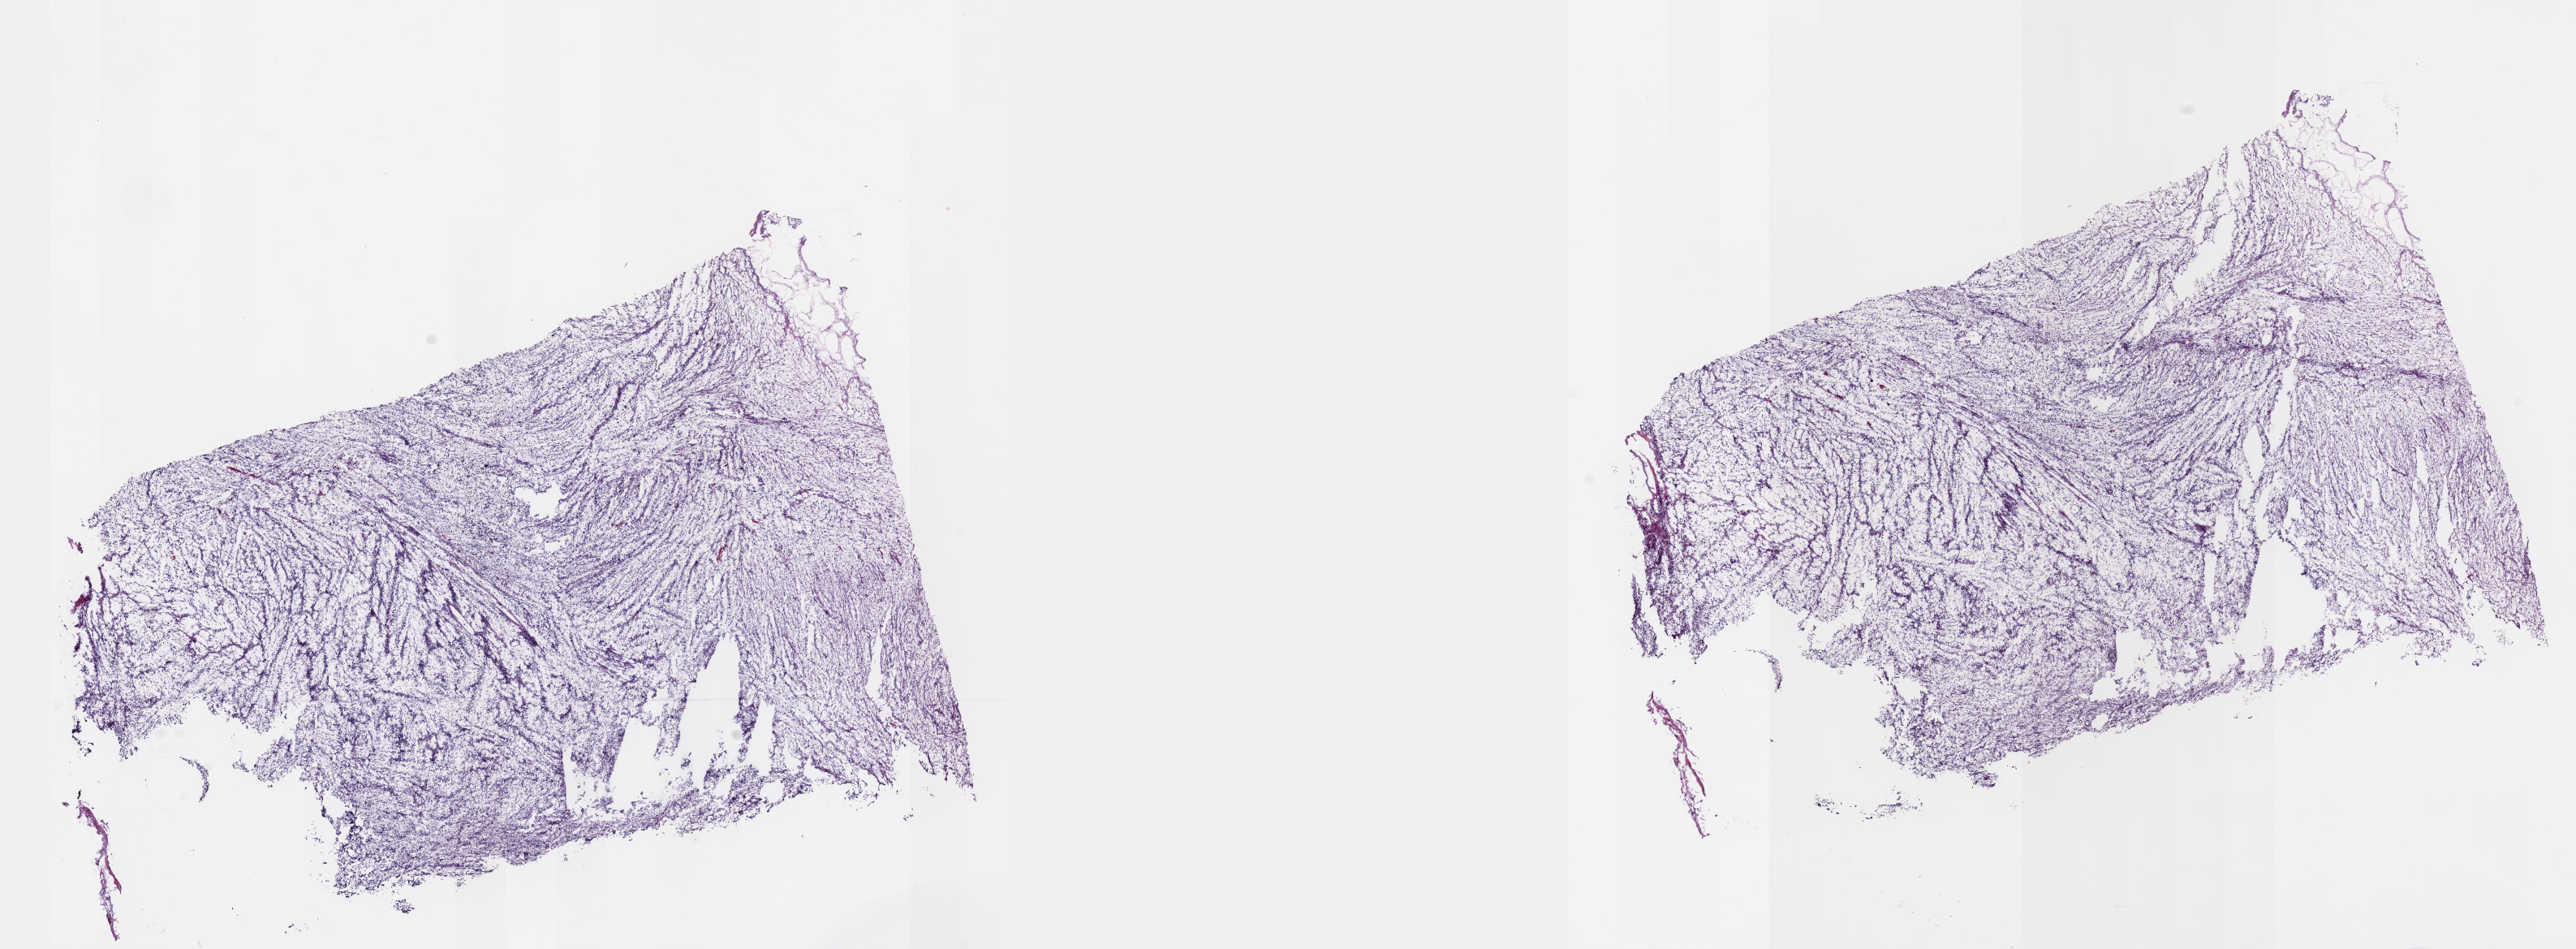
H&E-stained whole-slide image, a low-resolution overview of the entire scanned area, about 25.7 x 9.4 mm (slide scanned at 40x); frozen section from the top of the tissue portion; connective, subcutaneous and other soft tissues, primary tumour sample. Female, age 53 years at initial diagnosis. Slide review estimates, as recorded: tumour cells 100%, tumour nuclei 80%, normal cells 0%, stromal cells 0%, necrosis 0%. Inflammatory infiltration, as recorded: lymphocyte infiltration 1%, monocyte infiltration 0%, neutrophil infiltration 0%.
Diagnosis: Fibromyxosarcoma (connective, subcutaneous and other soft tissues of lower limb and hip).